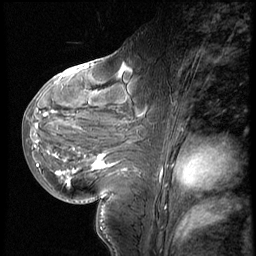
Breast MRI (dynamic contrast-enhanced), one sagittal slice; position 29 of 60 along the scan axis; 3 images stored at this slice position (order not interpretable as contrast timing); 1.5 T; TE 4.2 ms, TR 8.9 ms; 2.5 mm slice thickness; 256 × 256 image matrix. Patient: female, 29 years. Case-level facts recorded for this patient, not image findings: setting: breast cancer imaged before/during neoadjuvant chemotherapy.
Annotated regions visible in this slice (semi-automatic segmentation, software-assisted and operator-edited):
- analysis volume of interest (the breast-tissue region the enhancement analysis was run in; not a lesion): box from (x=29, y=57) to (x=153, y=200) px
- tumour enhancement mask (voxels above the 140 % enhancement threshold inside the analysis volume of interest): (x=37, y=66)–(x=128, y=180)